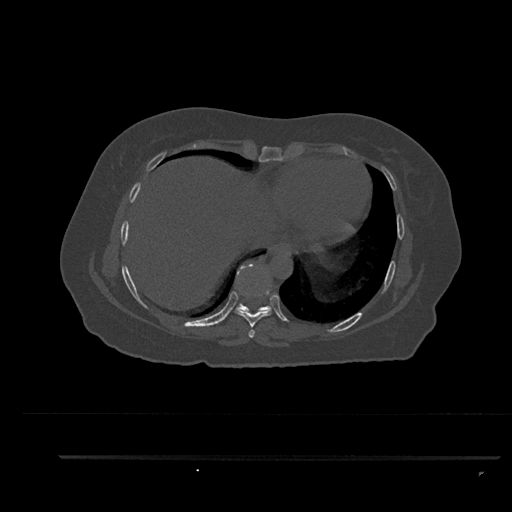
CT including the spine, one axial slice. Slice 445 of 797 in the series (ordered by position). Reconstruction kernel Br40s/3. Bone window (W 1800 / L 400 HU). 512 × 512 image matrix, field of view 408 × 408 mm. Female patient, age 44 years. From the clinical record (not read from this slice): primary cancer: renal; vertebrae with lytic lesions (as recorded): L1.
Annotated regions visible in this slice (semi-automatic segmentation, software-assisted and operator-edited):
- T7 vertebra: bounding box (x1, y1, x2, y2) in pixels: (248, 329, 255, 338)
- T8 vertebra: (235, 268, 272, 328)
- T9 vertebra: (234, 266, 272, 313)